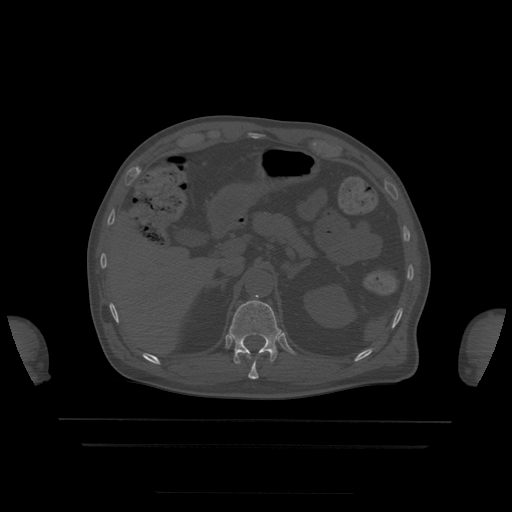
CT including the spine, one axial slice. Position 203 of 522 along the scan axis. Bone window (W 1800 / L 400 HU). 512 × 512 image matrix, field of view 436 × 436 mm. Patient age 68 years. Case-level facts recorded for this patient, not image findings: primary cancer: urothelial.
Structures marked on this image (semi-automatically segmented with operator editing):
- T11 vertebra: bounding box [x1, y1, x2, y2] px = [243, 353, 272, 380]
- T12 vertebra: [228, 295, 281, 364]